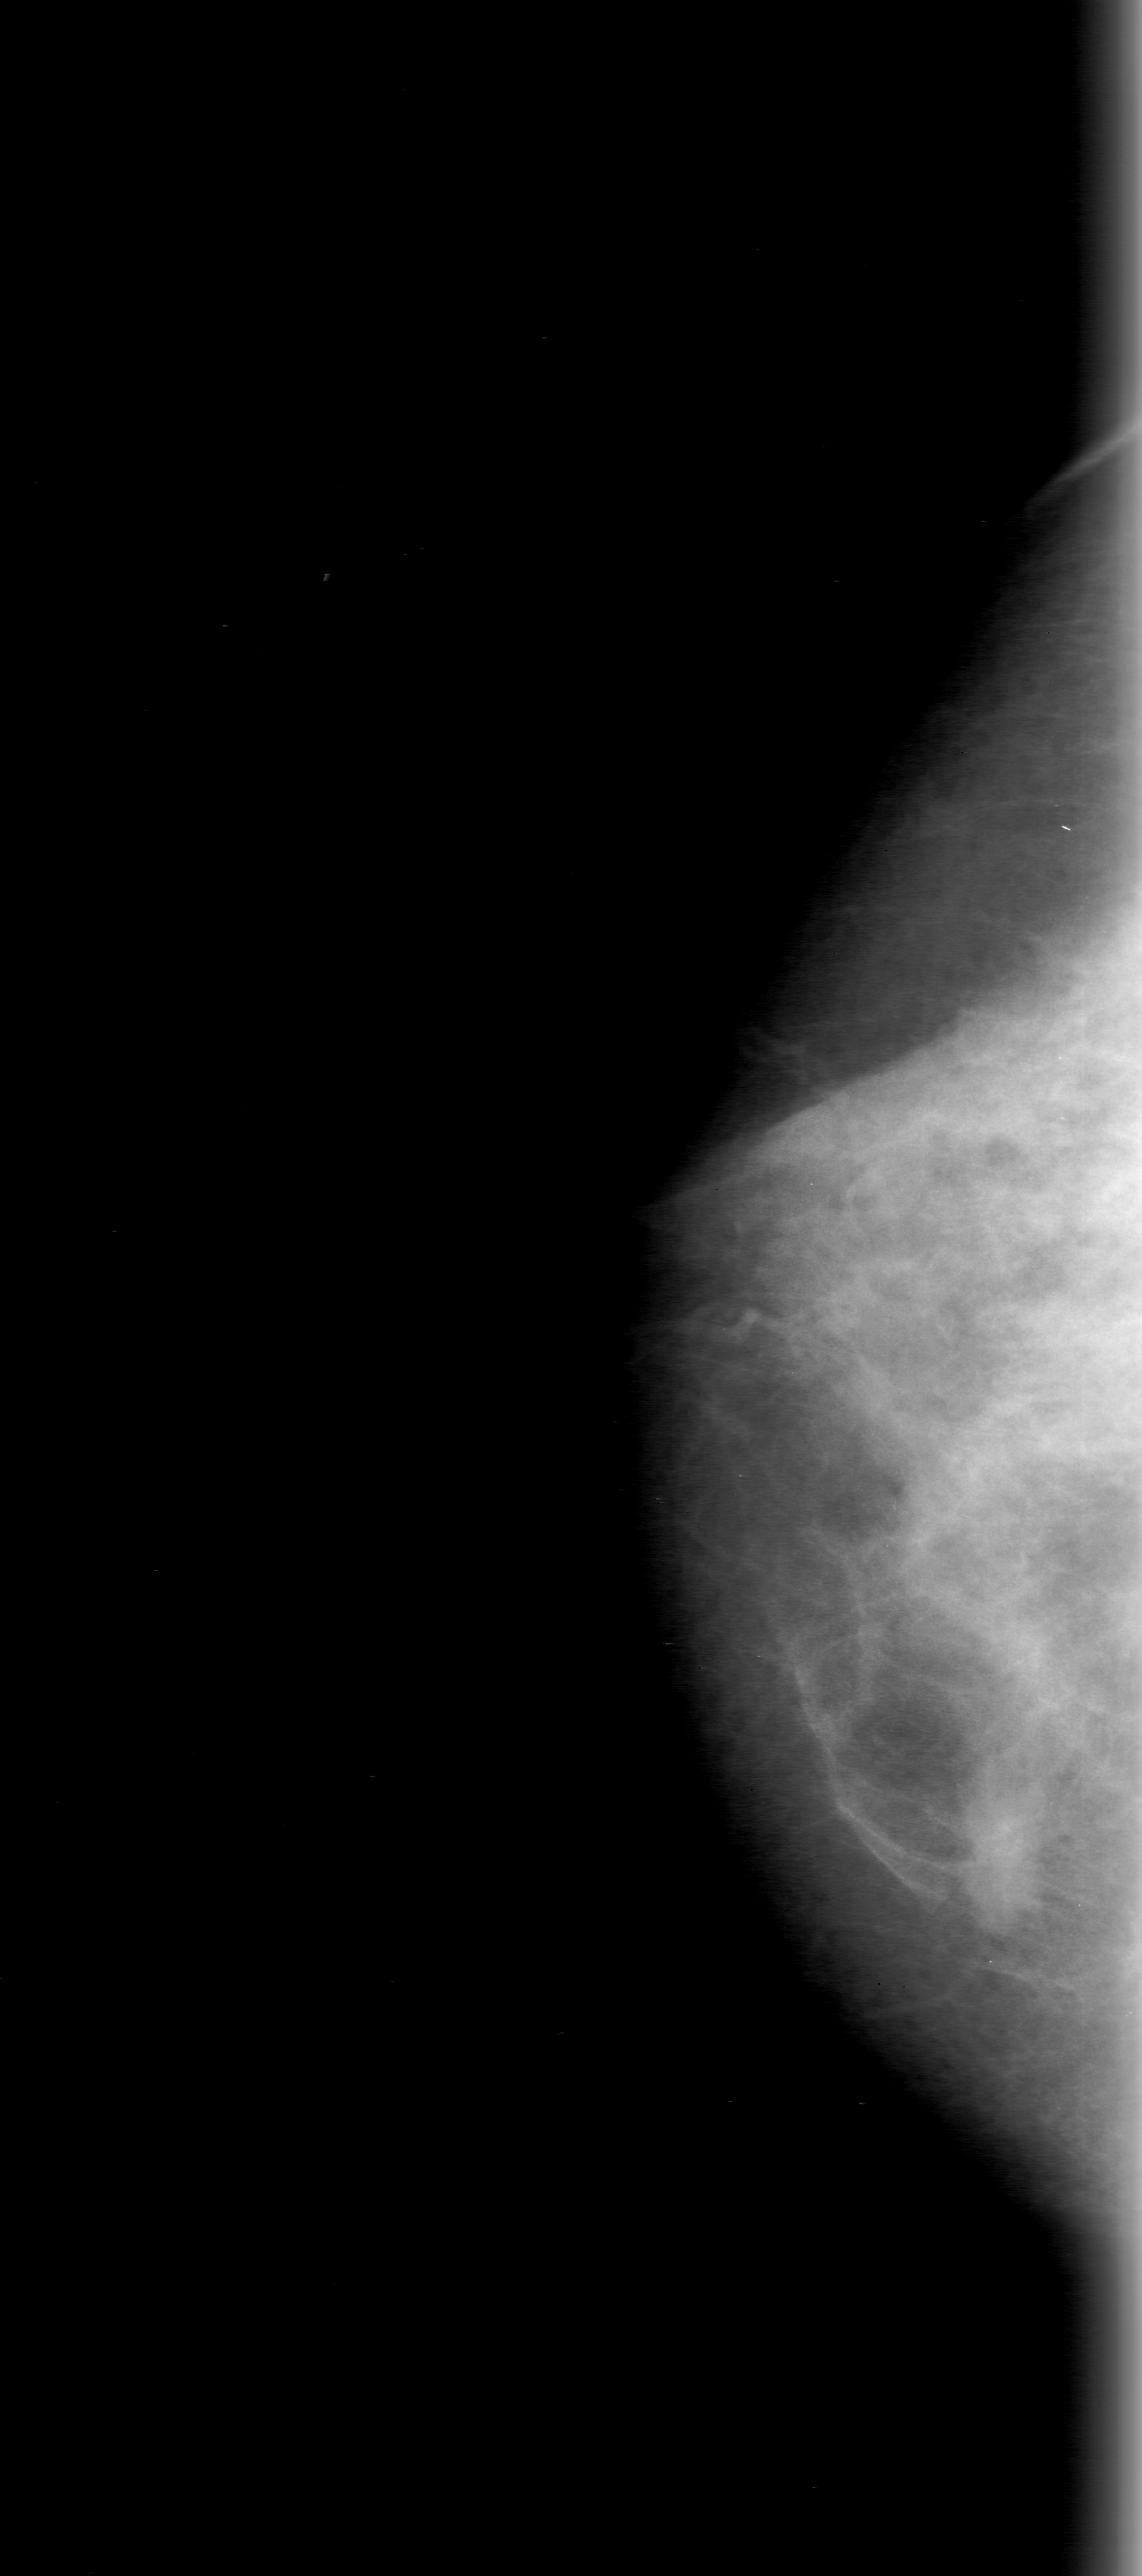
Digitized screen-film mammogram, right breast, craniocaudal (CC) view, breast composition: heterogeneously dense (BI-RADS density category 3 of 4).
Radiologist-marked abnormalities on this image: mass, shape irregular, margins ill defined; BI-RADS assessment category 0; pathology result (as recorded, not read from the image): malignant.